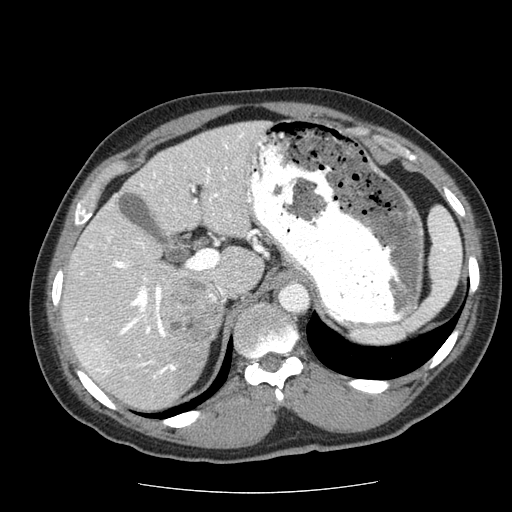
Contrast-enhanced abdominal CT (liver protocol), one axial slice. Position 38 of 85 along the scan axis. Reconstruction kernel STANDARD. Soft-tissue window (W 400 / L 40 HU). 2.5 mm slice thickness. 512 × 512 image matrix, field of view 360 × 360 mm. From the clinical record (not read from this slice): diagnosis: hepatocellular carcinoma (patient treated with transarterial chemoembolisation; whether this scan precedes or follows treatment is not stated here); TNM stage (as recorded): Stage-IIIA; Child-Pugh class: A; tumour nodularity: multinodular; tumour size: 8 cm.
Outlined on this slice (semi-automatic segmentation, software-assisted and operator-edited):
- abdominal aorta: bounding box (x1, y1, x2, y2) in pixels: (279, 283, 309, 312)
- liver parenchyma outside the tumour (the mass and vessels are separate outlines, so this box may not span the whole liver): (62, 120, 269, 410)
- mass: (161, 274, 223, 342)
- liver vessels: (79, 133, 261, 378)